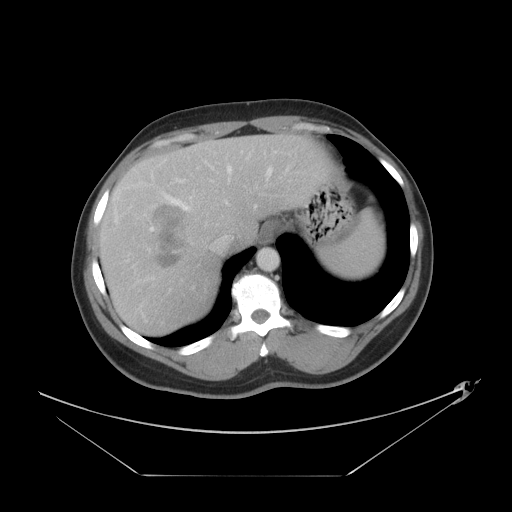
Contrast-enhanced abdominal CT, one axial slice. Slice 33 of 44 in the series (ordered by position). Reconstruction kernel STANDARD. Intravenous contrast given. Soft-tissue window (W 400 / L 40 HU). 5 mm slice thickness. 512 × 512 image matrix. Male patient, age 49 years. From the clinical record (not read from this slice): diagnosis: colorectal cancer liver metastases, imaged before liver resection; multiple liver metastases: no.
Annotated regions visible in this slice (manually delineated by an expert):
- hepatic veins: bounding box <163,165,290,249> (left, top, right, bottom; pixels)
- liver: <100,135,336,336>
- planned liver remnant (the part of the liver to remain after resection): <193,134,336,248>
- portal vein (with intrahepatic branches): <115,180,183,231>
- liver metastasis: <154,205,185,267>